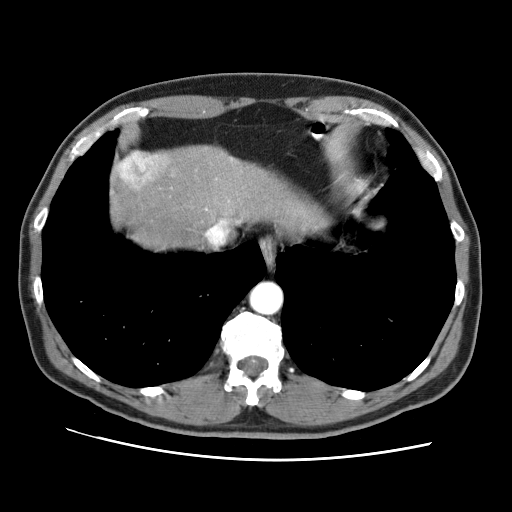
Contrast-enhanced abdominal CT (liver protocol), one axial slice; slice 62 of 71 in the series (ordered by position); reconstruction kernel STANDARD; 120 kVp; soft-tissue window (W 400 / L 40 HU); 512 × 512 image matrix. Case-level facts recorded for this patient, not image findings: diagnosis: hepatocellular carcinoma (patient treated with transarterial chemoembolisation; whether this scan precedes or follows treatment is not stated here); TNM stage (as recorded): Stage-II; Child-Pugh class: A; tumour differentiation: well differentiated; tumour nodularity: multinodular.
Annotated regions visible in this slice (semi-automatic segmentation, software-assisted and operator-edited):
- liver parenchyma outside the tumour (the mass and vessels are separate outlines, so this box may not span the whole liver): bounding box (x1, y1, x2, y2) in pixels: (114, 146, 326, 249)
- mass: (119, 153, 170, 201)